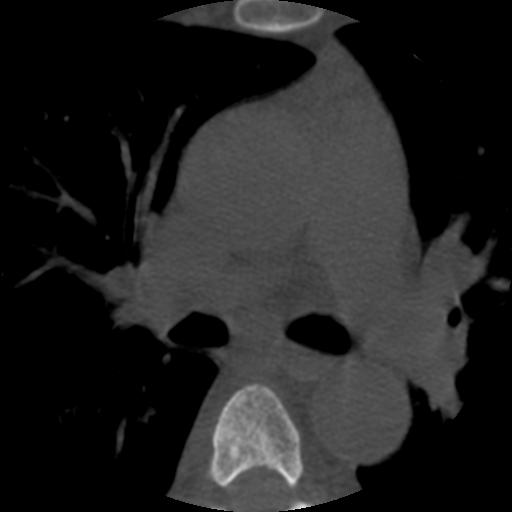
CT including the spine, one axial slice; position 374 of 508 along the scan axis; 120 kVp; bone window (W 1800 / L 400 HU); 1.25 mm slice thickness; 512 × 512 image matrix, field of view 160 × 160 mm. Patient age 57 years. Case-level facts recorded for this patient, not image findings: primary cancer: prostate.
Outlined on this slice (semi-automatic segmentation, software-assisted and operator-edited):
- T5 vertebra: box from (x=207, y=384) to (x=311, y=508) px
- T6 vertebra: (x=211, y=501)–(x=304, y=512)